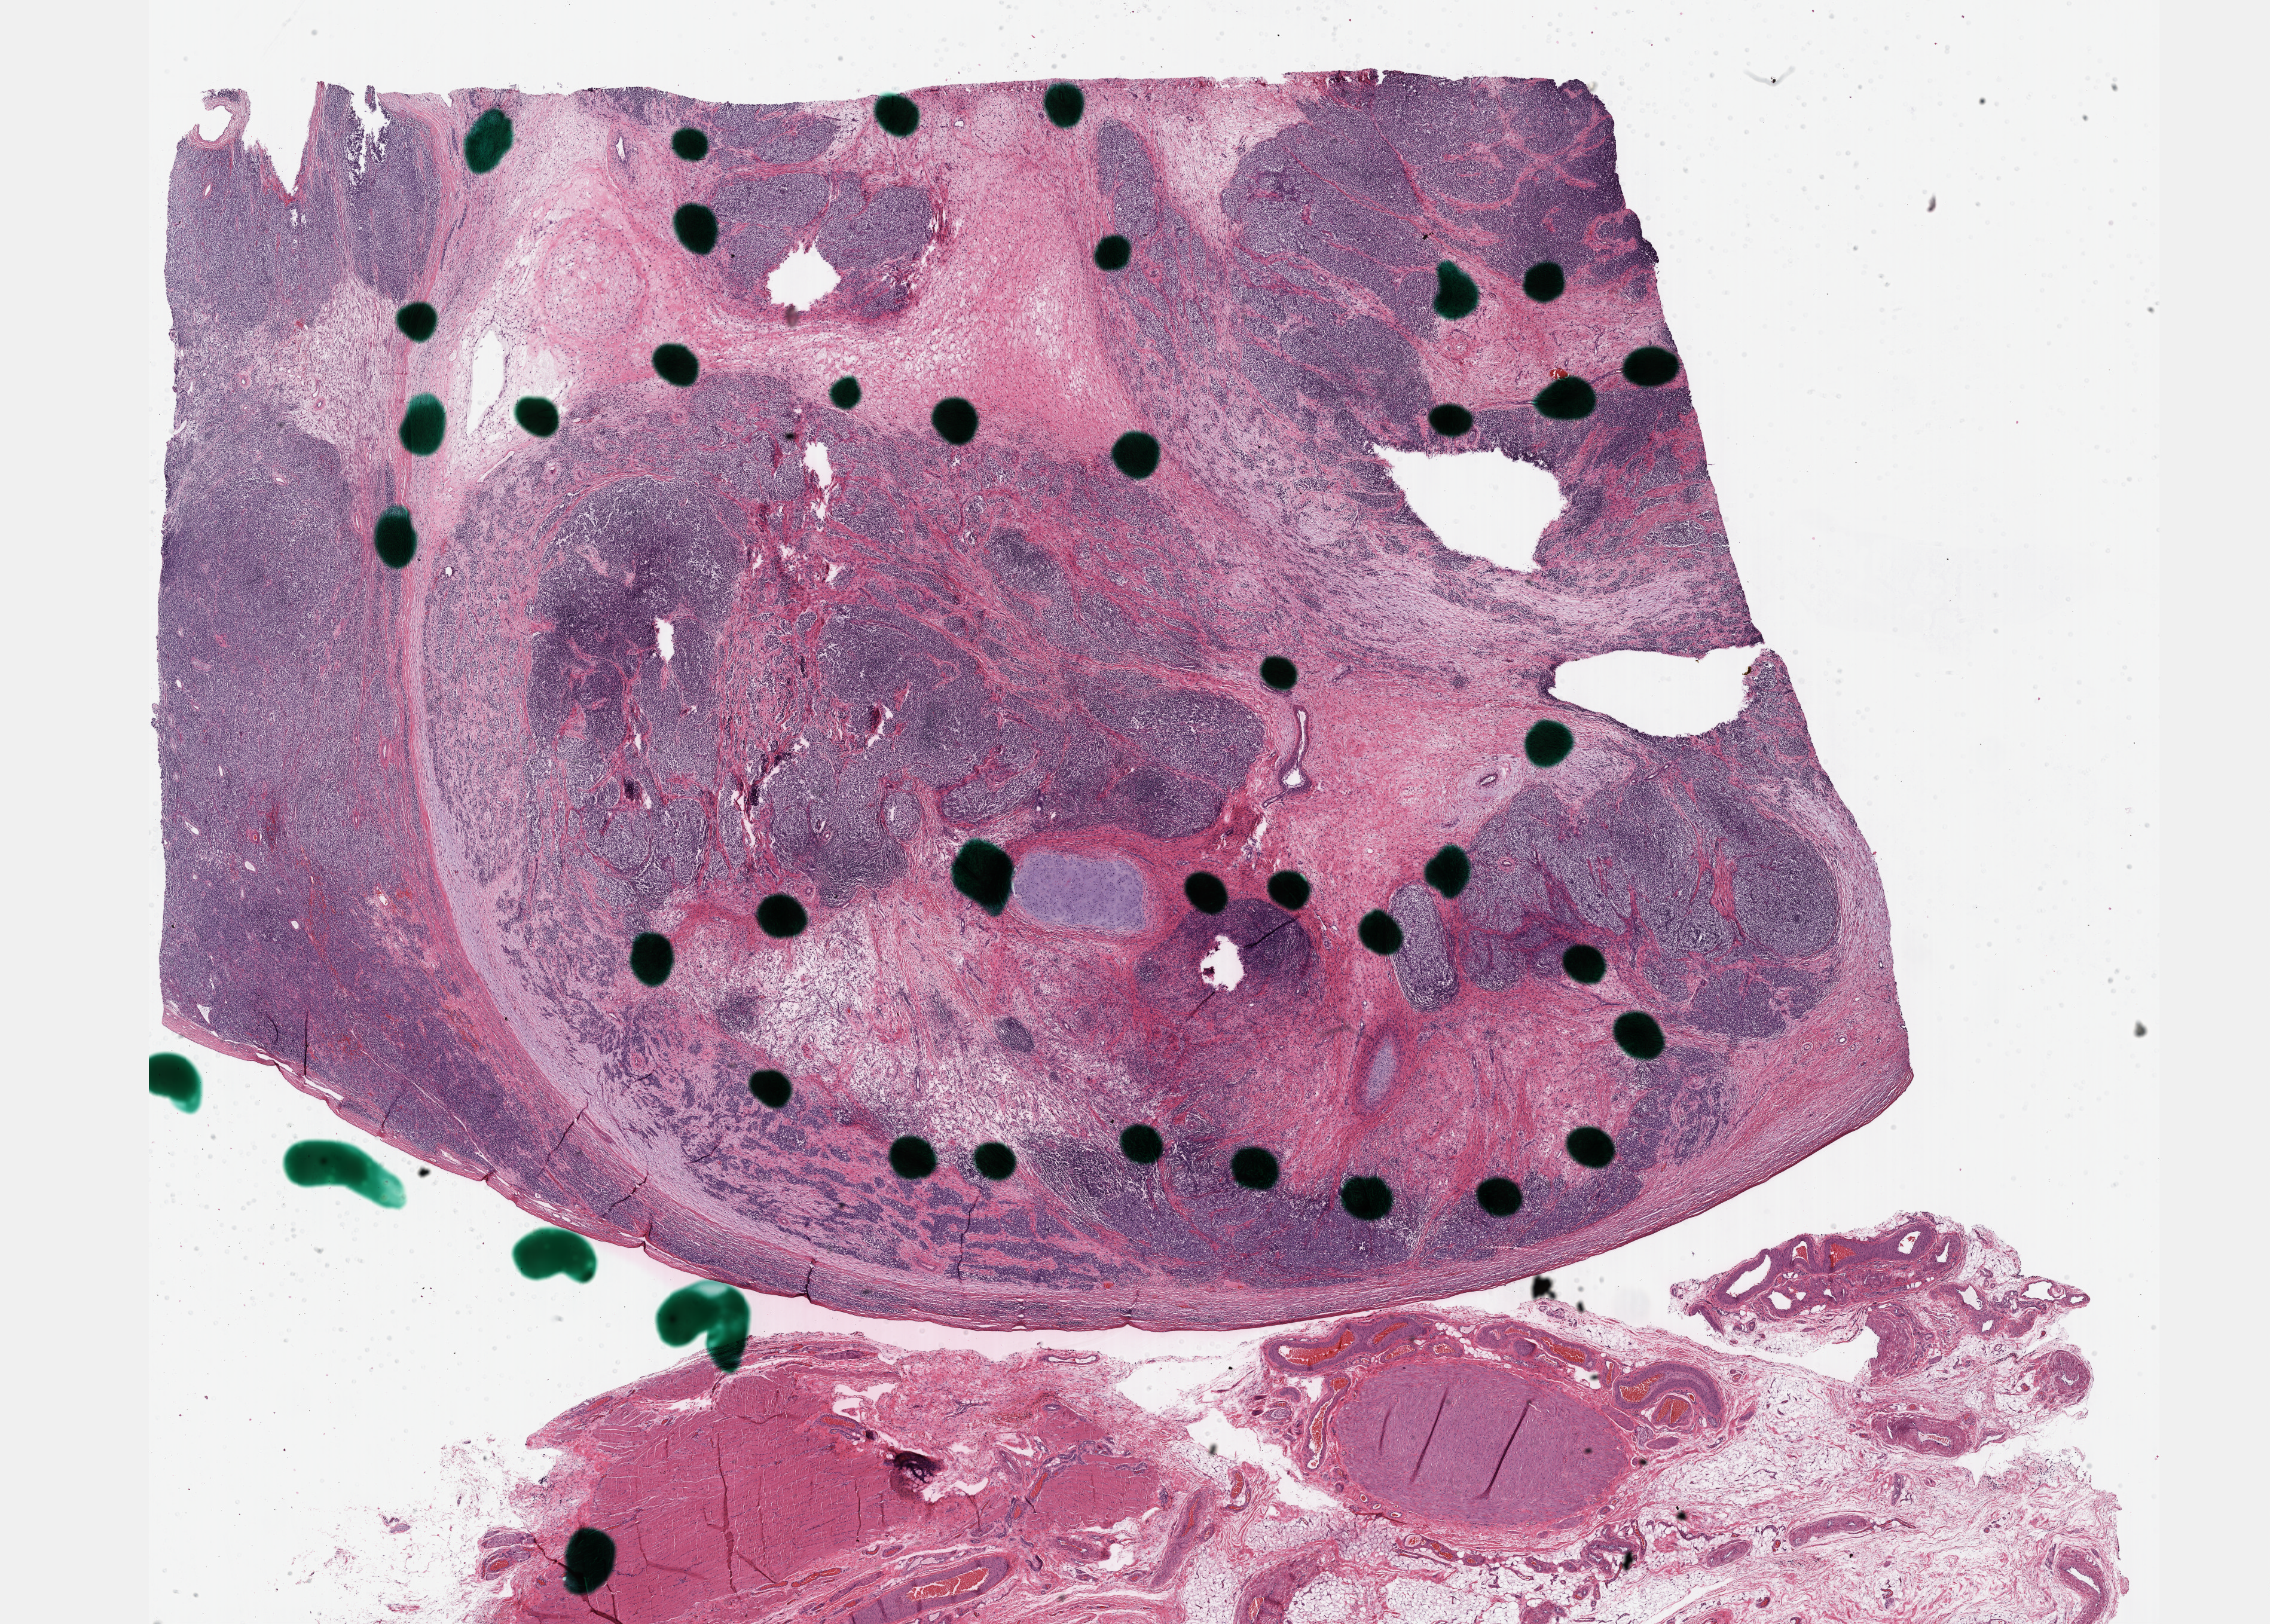
Whole-slide histology image, H&E-stained, low-resolution overview of the scanned area, about 30.7 x 22.0 mm (acquisition: 40x scan), formalin-fixed paraffin-embedded (FFPE) diagnostic section, testis, primary tumour sample. Patient: male, age at initial diagnosis 26 years.
AJCC pathologic stage: IS (7th edition). Pathologic diagnosis: Mixed germ cell tumor.